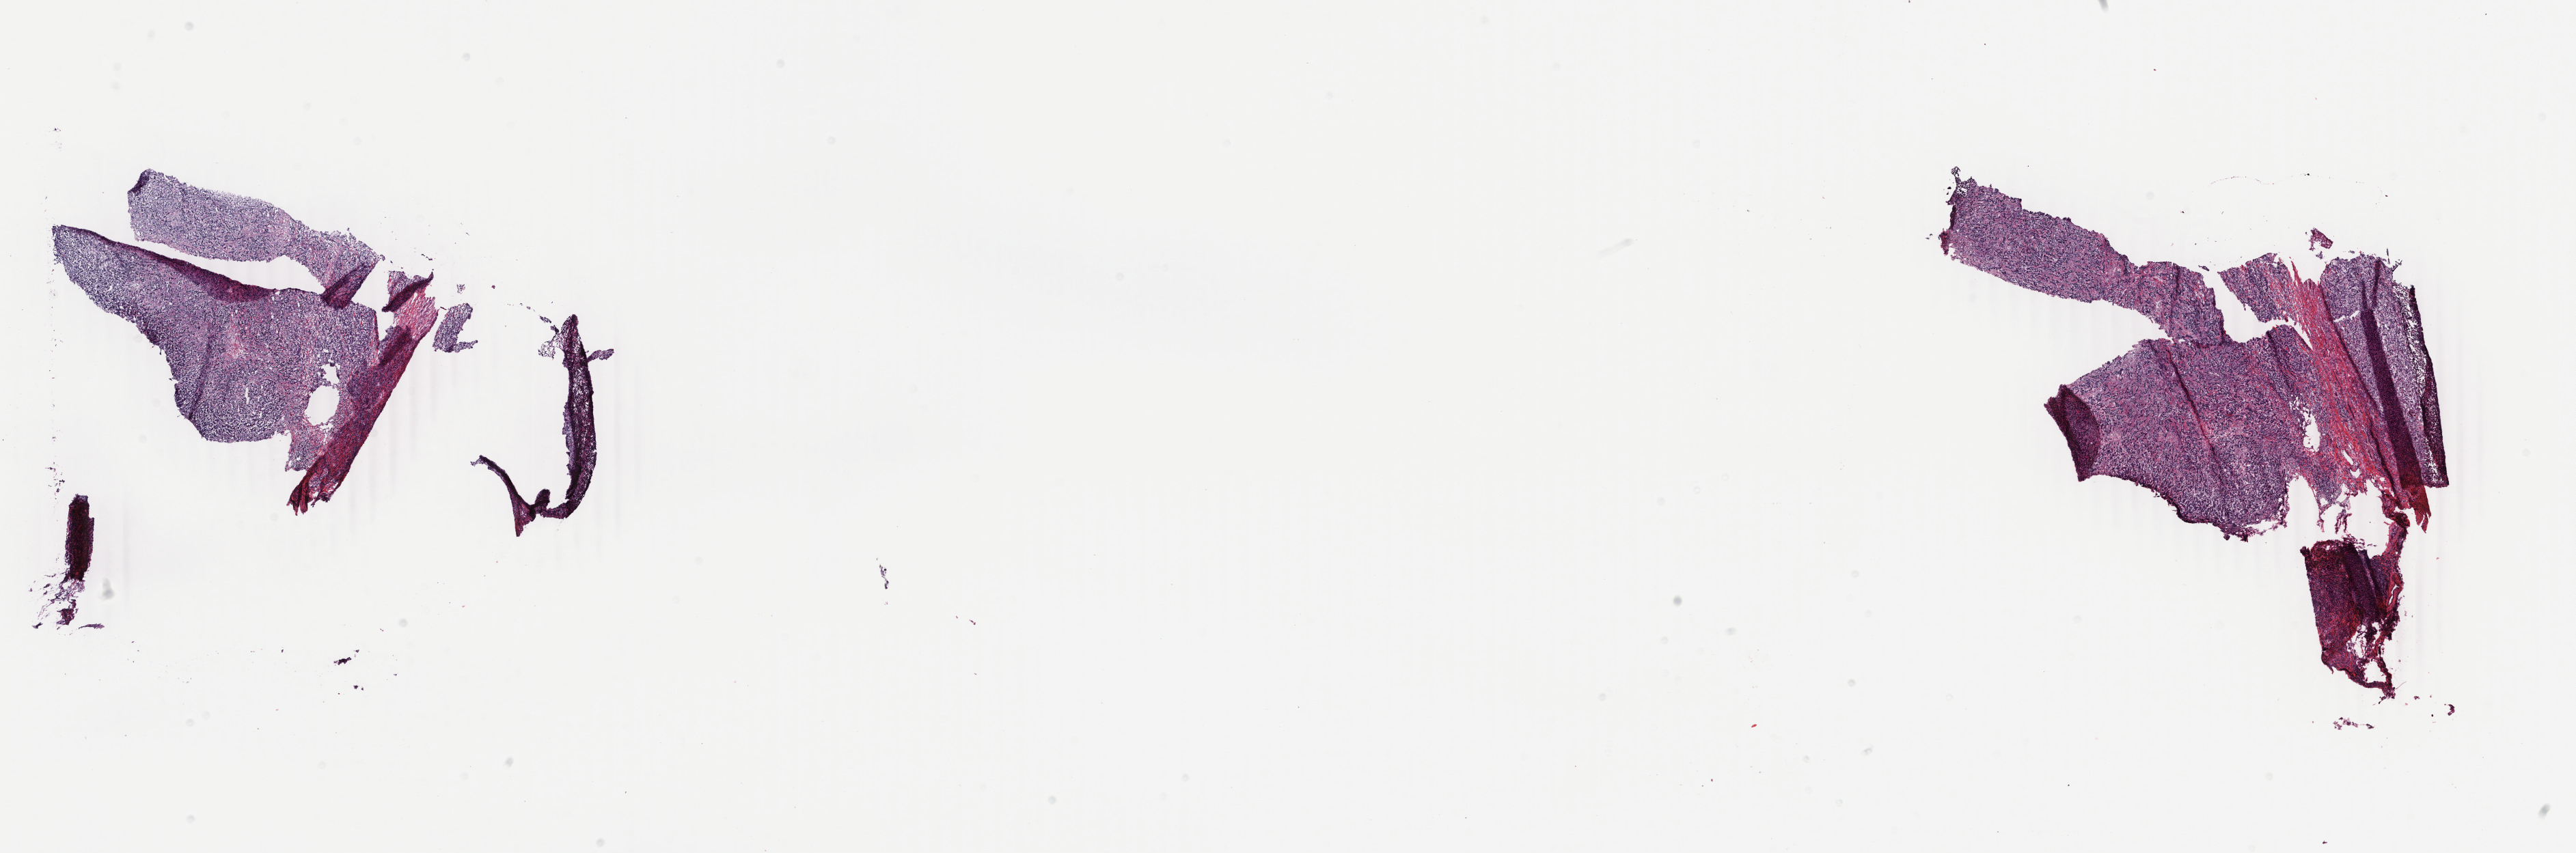
Whole-slide histology image, H&E-stained — low-resolution overview of the scanned area, about 30.0 x 9.9 mm; frozen section from the bottom of the tissue portion; sample: primary tumour, breast. Female patient; age at initial diagnosis 53 years. Pathologist review of this section (percent, as recorded): tumour cells 80%, tumour nuclei 80%, normal cells 0%, stromal cells 18%, necrosis 2%. Infiltration values recorded for this section: lymphocyte infiltration 2%, monocyte infiltration 1%, neutrophil infiltration 1%.
Histologic diagnosis: Infiltrating duct carcinoma, NOS. Lymph nodes positive (case pathology): 5 of 19 examined. Laterality: right. AJCC pathologic stage: IIIA.